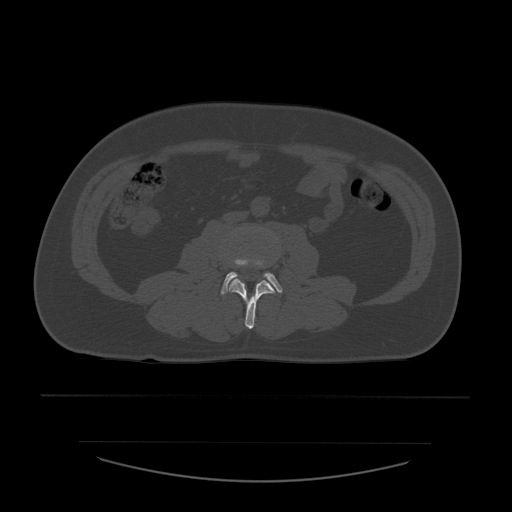
CT including the spine, one axial slice. Slice 162 of 532 in the series (ordered by position). Reconstruction kernel STANDARD. Bone window (W 1800 / L 400 HU). 1.25 mm slice thickness. 512 × 512 image matrix. Patient age 44 years. From the clinical record (not read from this slice): primary cancer: soft tissue sarcoma.
Structures marked on this image (semi-automatic segmentation, software-assisted and operator-edited):
- L3 vertebra: bounding box <229,233,274,329> (left, top, right, bottom; pixels)
- L4 vertebra: <221,259,283,295>